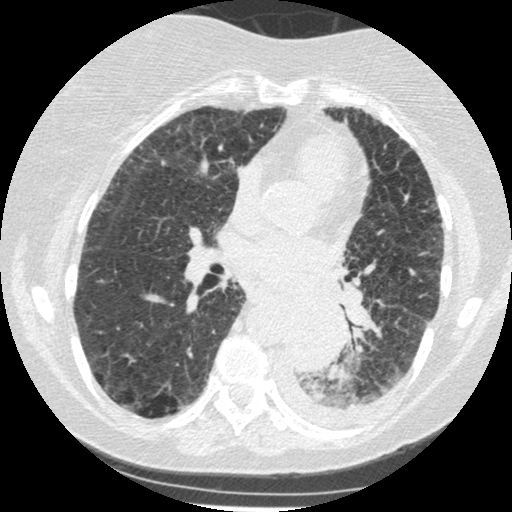
Low-dose screening chest CT, one axial slice. Position 122 of 341 along the scan axis. Lung window (W 1500 / L -600 HU). 1.25 mm slice thickness. 512 × 512 image matrix, field of view 310 × 310 mm.
Annotated regions visible in this slice (outlined manually by an expert reader):
- lesion 1 (tumor, lower lobe of left lung): bounding box <284,301,345,373> (left, top, right, bottom; pixels)